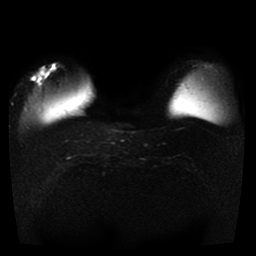
Breast MRI, one axial slice; position 10 of 41 along the scan axis; diffusion-weighted series; image 2 of 4 stored at this slice position (different b-values; order by instance number); 1.5 T; 256 × 256 image matrix, field of view 330 × 330 mm. Female patient.
Structures marked on this image (manually delineated by an expert):
- tumour on diffusion-weighted imaging: bounding box (x1, y1, x2, y2) in pixels: (34, 69, 46, 81)